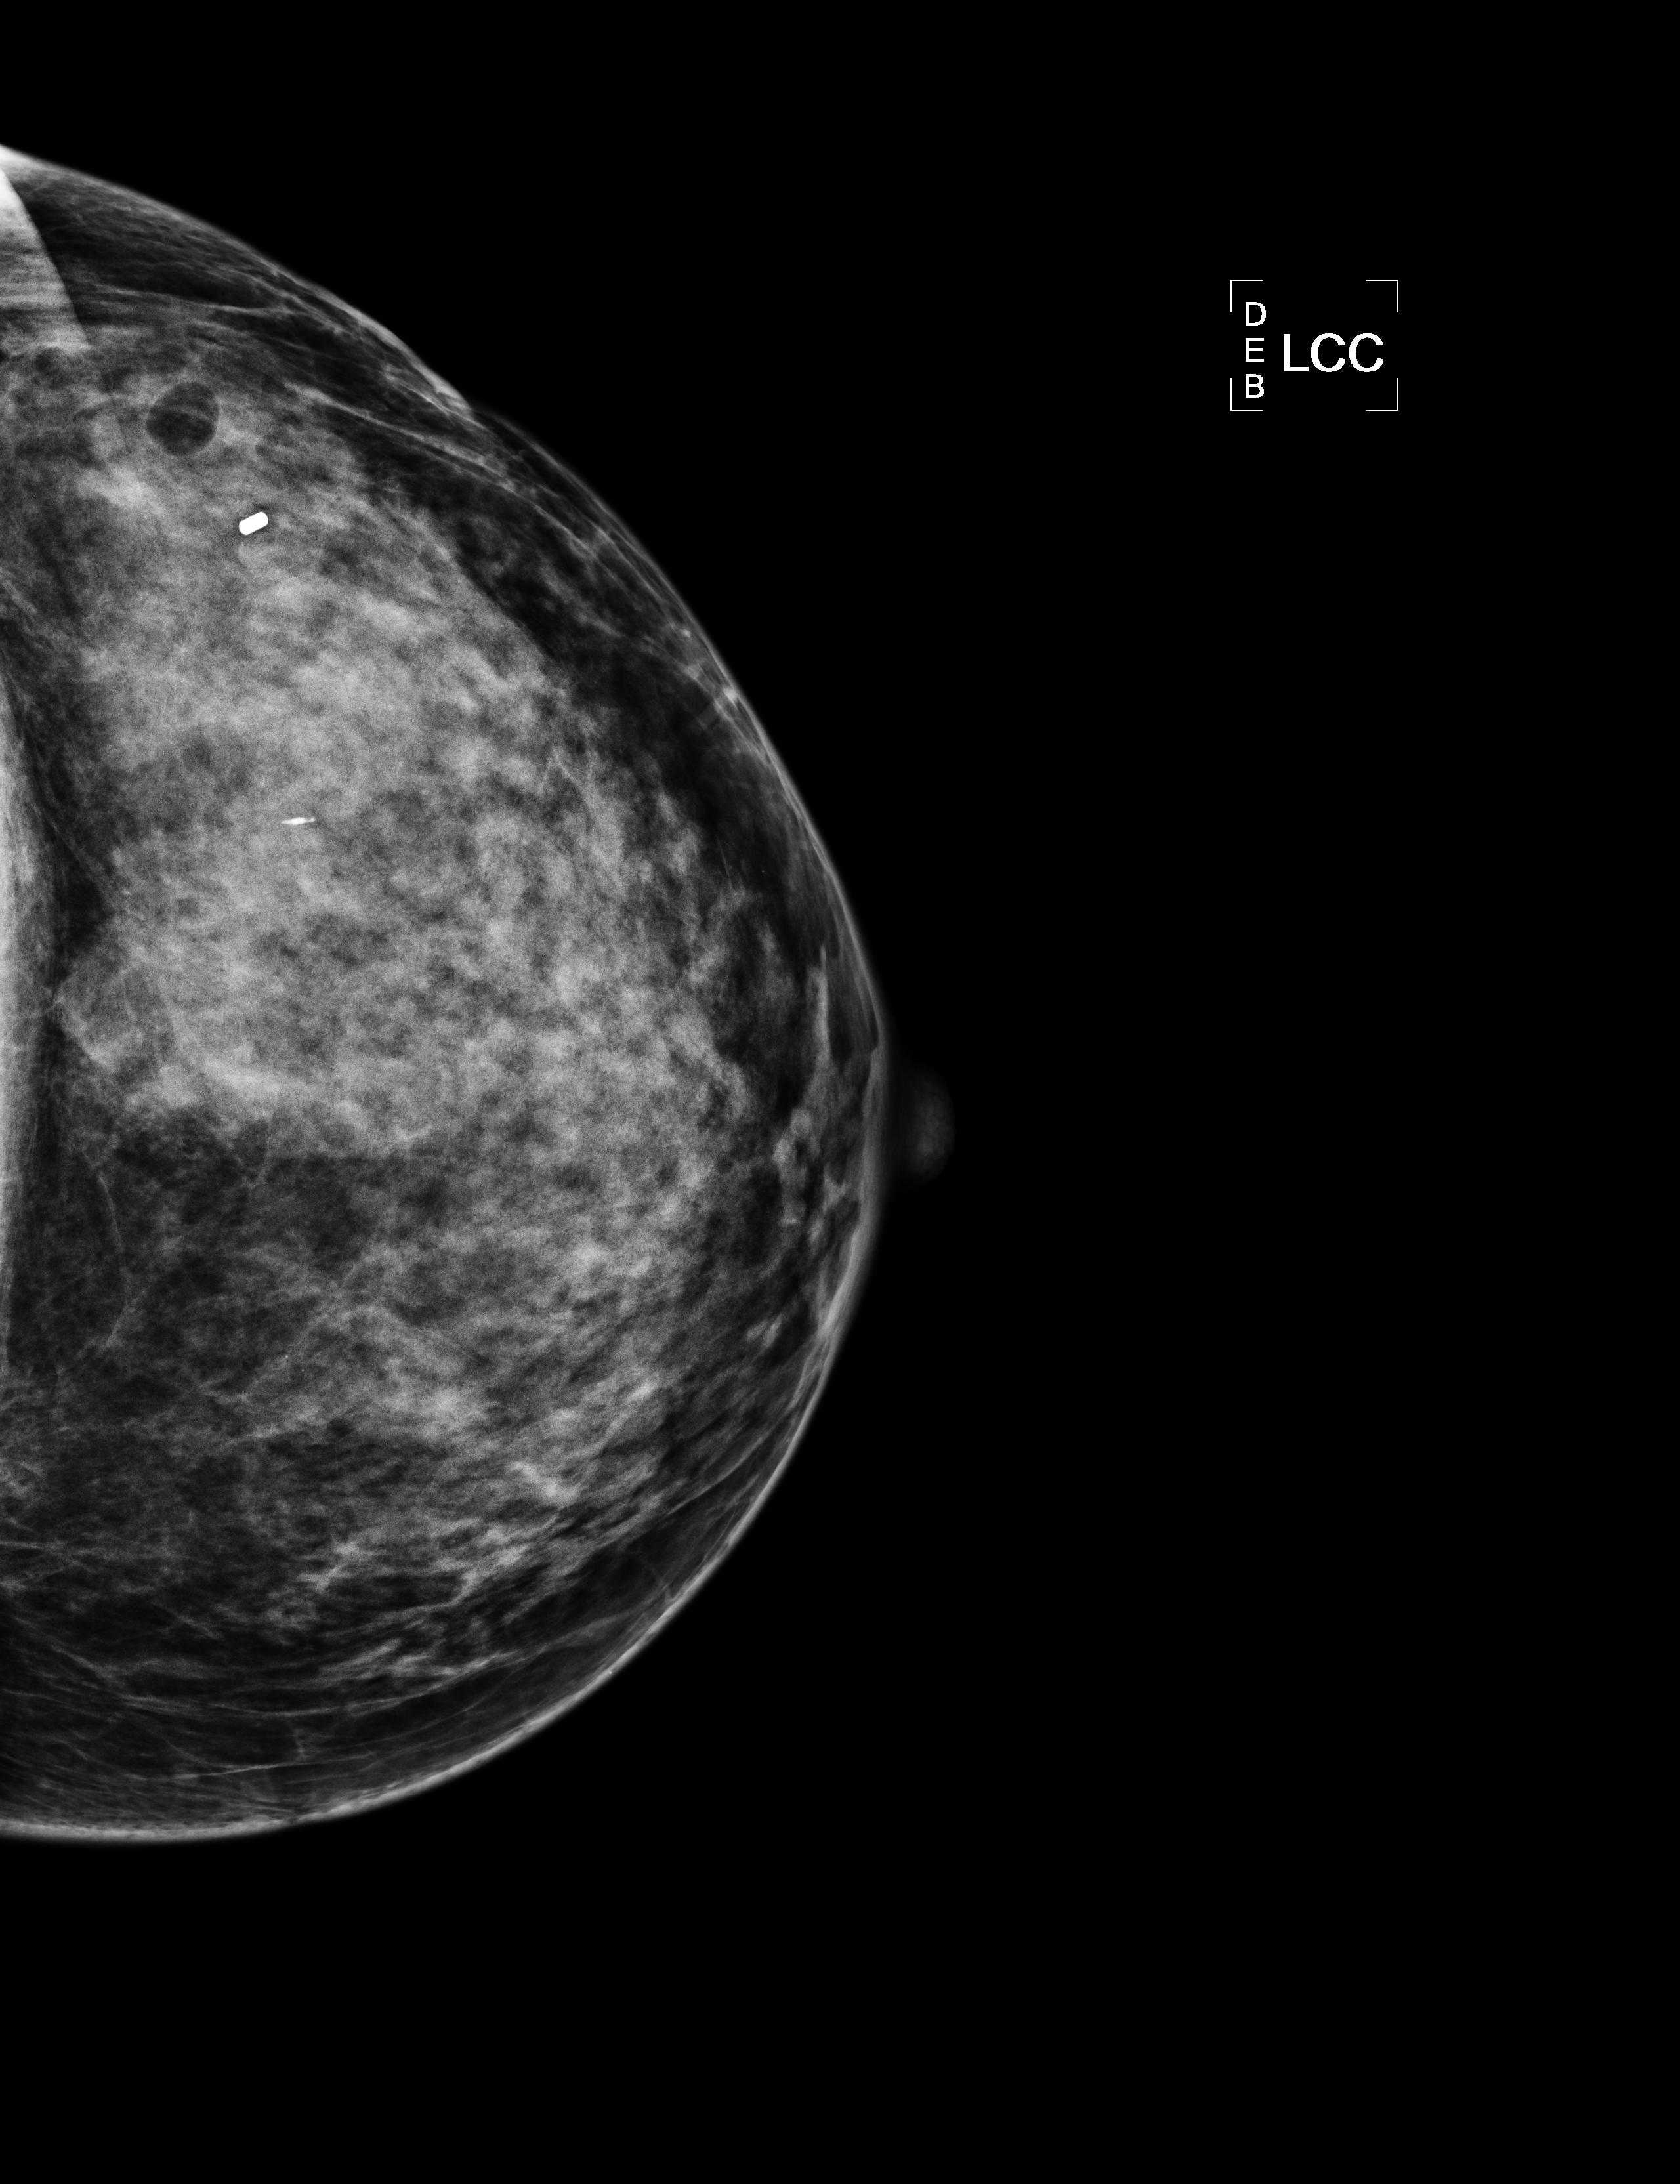
Mammogram, left breast, CC view.
Patient-level pathology facts (clinical record, not image findings): pathology diagnosis: benign fibrocyst (left breast).